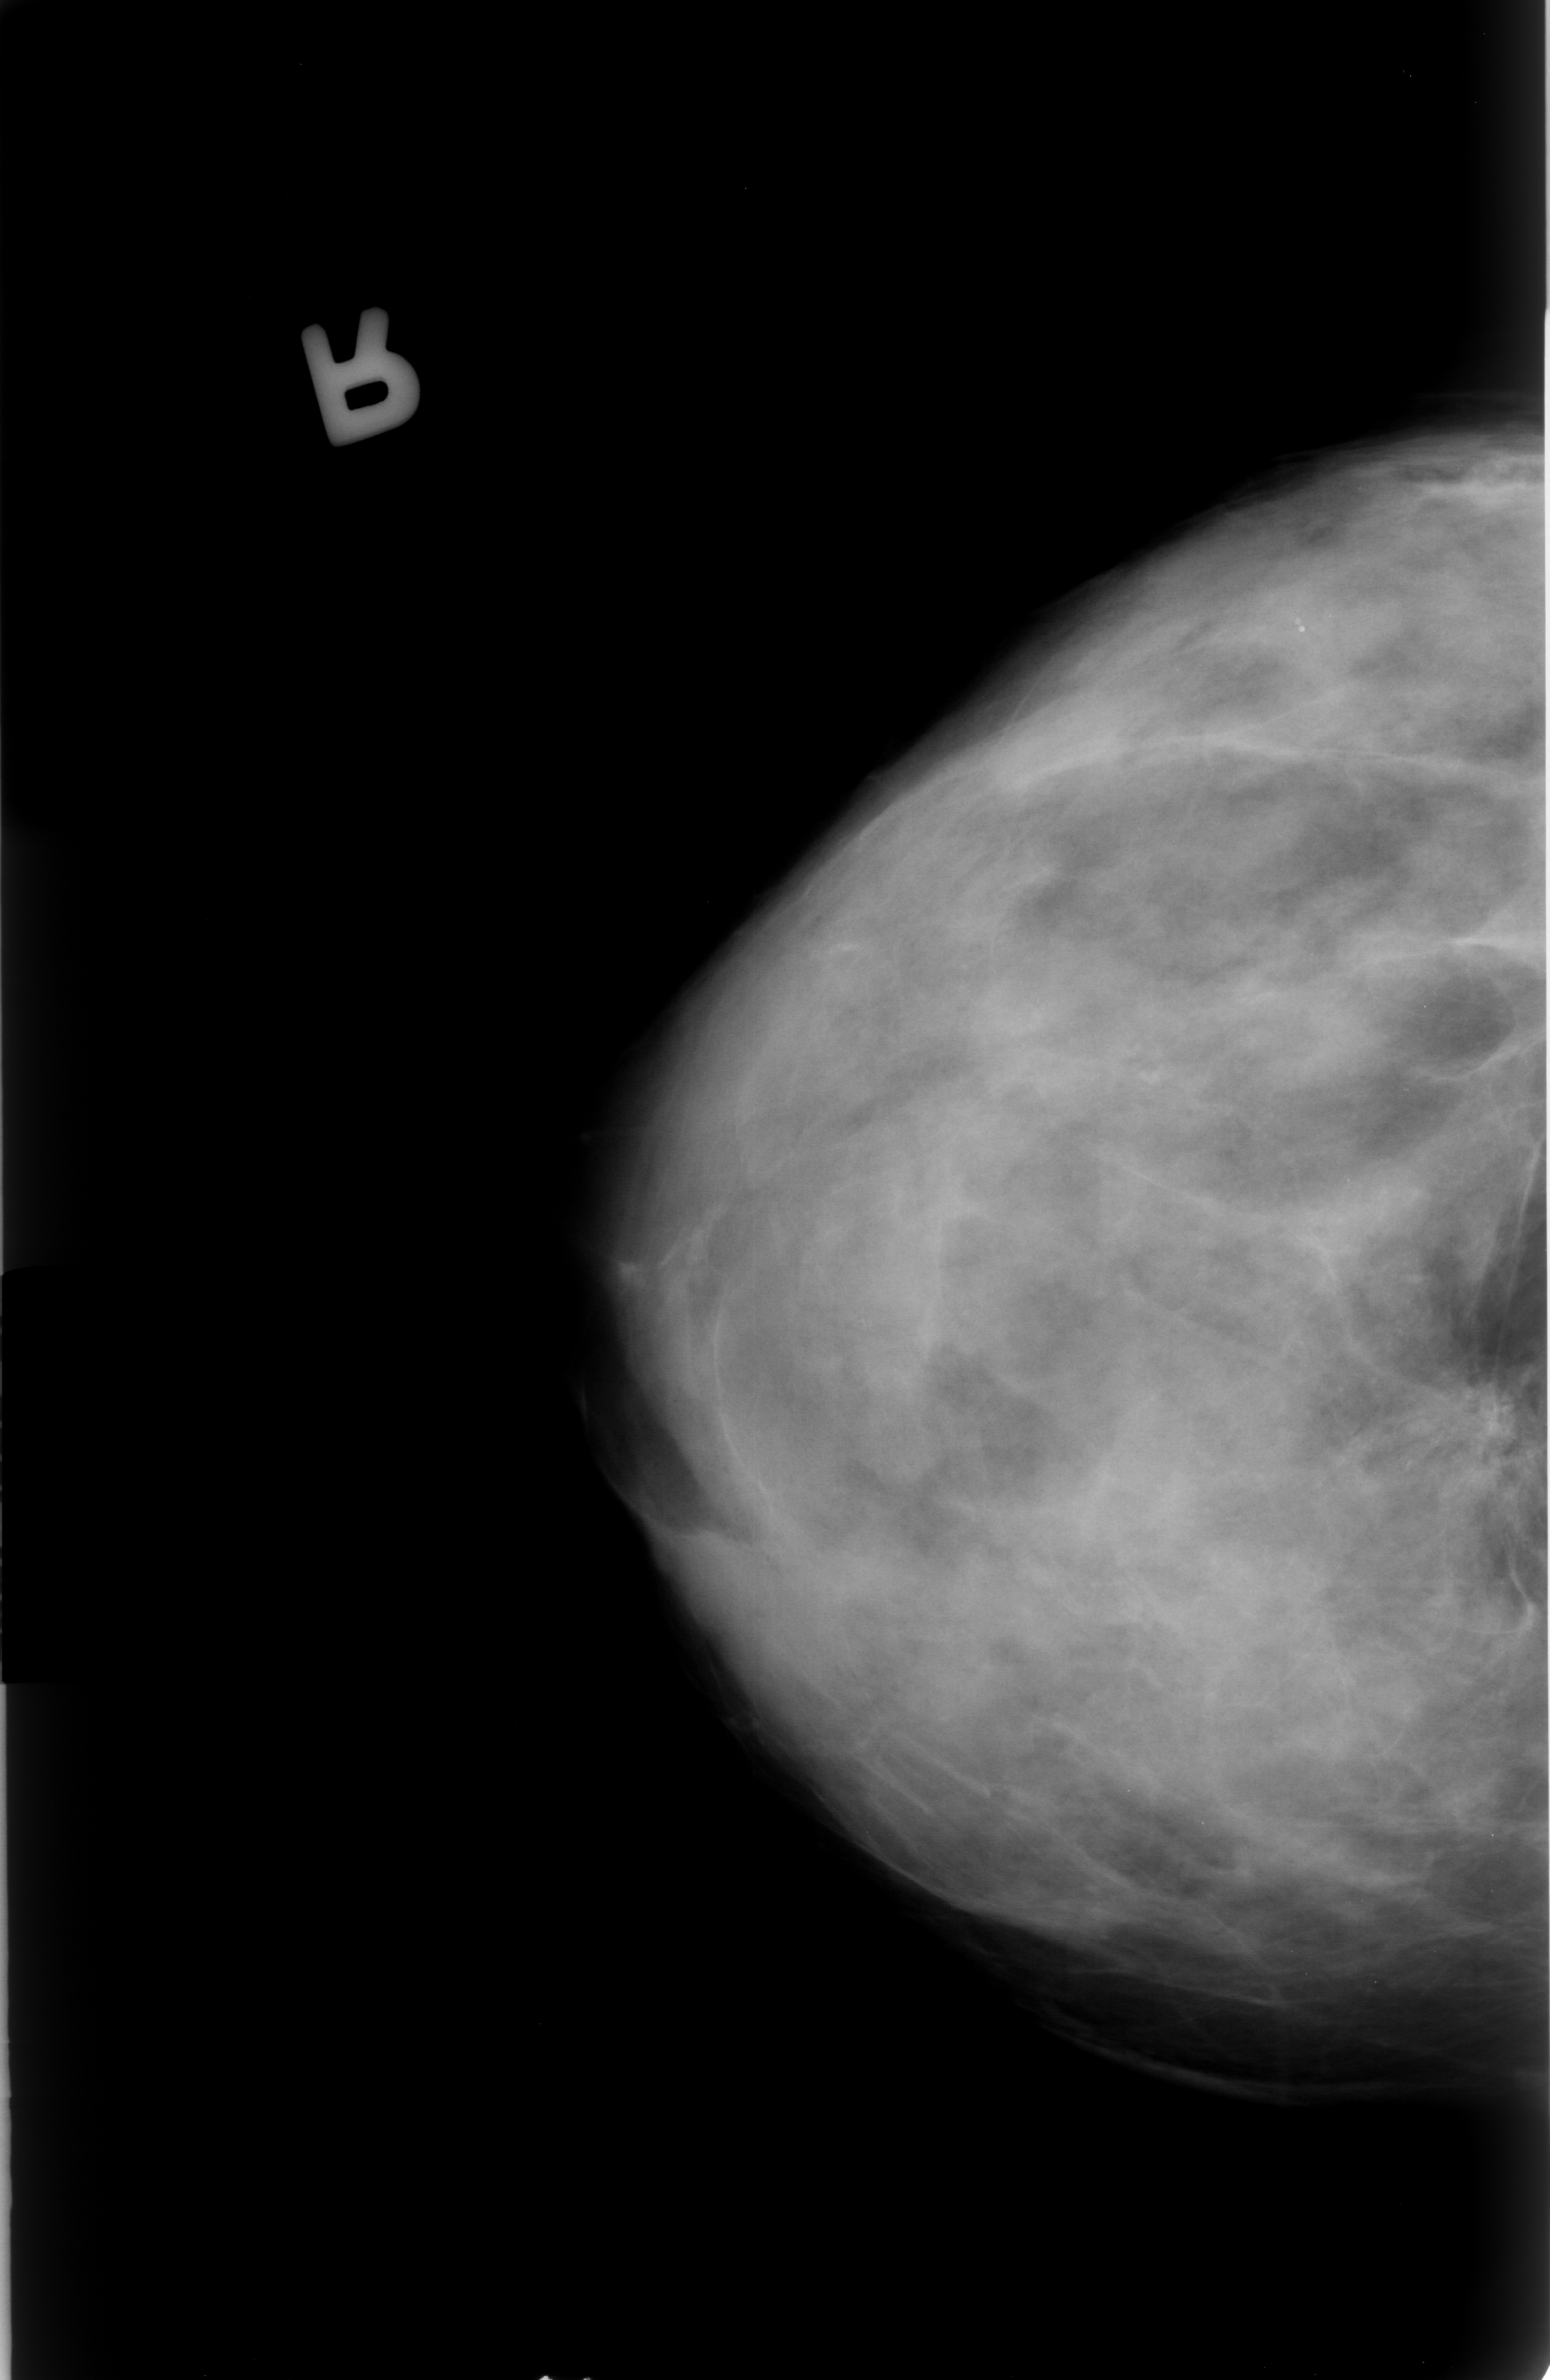
Mammogram (digitized film); right breast; craniocaudal (CC) view; 1550 × 2380 image matrix.
Expert-marked regions of interest on this film, with their recorded descriptors:
- calcifications, morphology punctate / pleomorphic, distribution clustered; BI-RADS assessment category 4; subtlety rating 3 on a 1 (subtle) to 5 (obvious) scale; pathology result (as recorded, not read from the image): malignant: bounding box <1287,1295,1547,1589> (left, top, right, bottom; pixels)